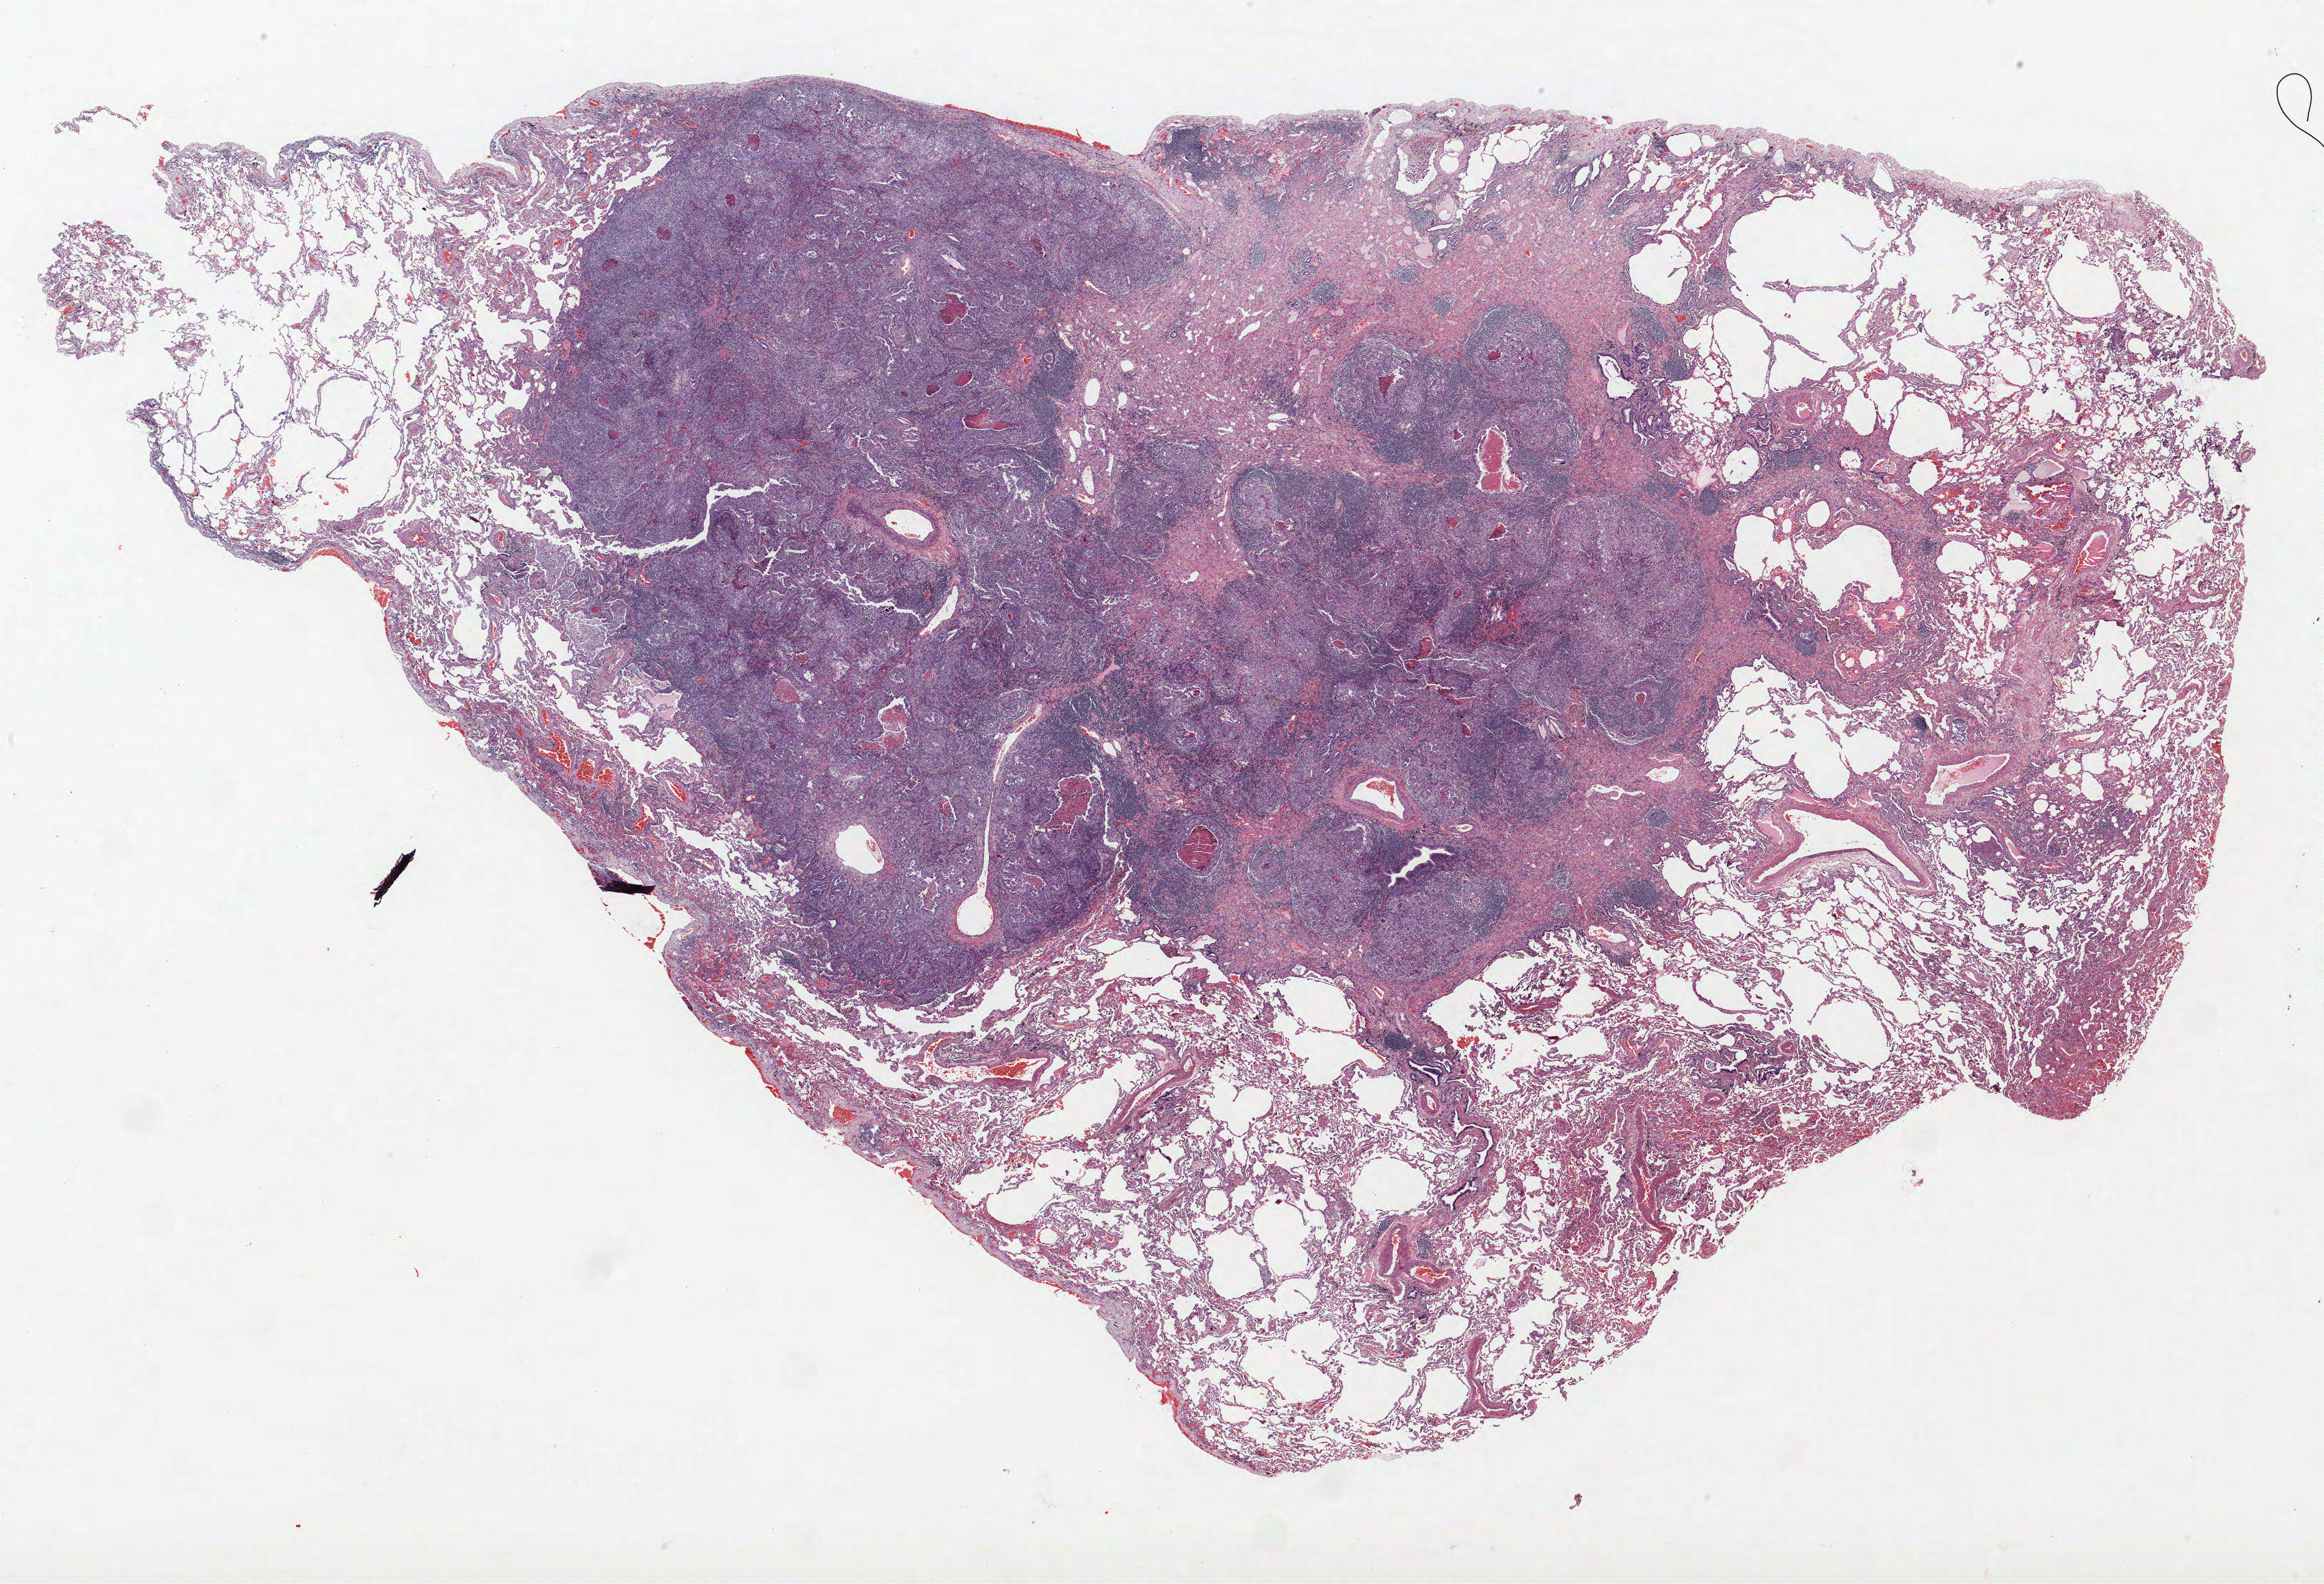
Whole-slide histology image, H&E-stained — shown as a low-resolution overview of the whole scanned area (about 29.8 x 20.3 mm); FFPE section; lung tissue. Male, age 58 at enrolment. Current smoker at enrolment. Grade: moderately differentiated (G2).
Tumour size (pathology): 28 mm. Stage (AJCC 6th edition): IA. ICD-O-3 topography: lower lobe of lung (C34.3). Primary tumour location (clinical record): left lower lobe. Participant's lung-cancer diagnosis: Adenosquamous carcinoma (ICD-O-3 8560/3).